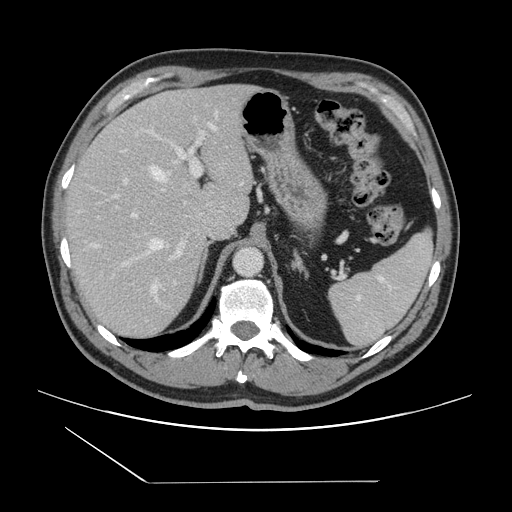
Contrast-enhanced abdominal CT, one axial slice; position 101 of 157 along the scan axis; 120 kVp; intravenous contrast given; soft-tissue window (W 400 / L 40 HU); 2.5 mm slice thickness; 512 × 512 image matrix, field of view 407 × 407 mm. Male patient, age 61 years. Case-level facts recorded for this patient, not image findings: diagnosis: colorectal cancer liver metastases, imaged before liver resection; multiple liver metastases: yes; largest metastasis: 5.5 cm; disease in both lobes: yes.
Outlined on this slice (manually delineated by an expert):
- hepatic veins: bounding box [x1, y1, x2, y2] px = [150, 124, 216, 293]
- liver: [67, 85, 252, 339]
- planned liver remnant (the part of the liver to remain after resection): [68, 85, 238, 225]
- portal vein (with intrahepatic branches): [93, 129, 205, 264]